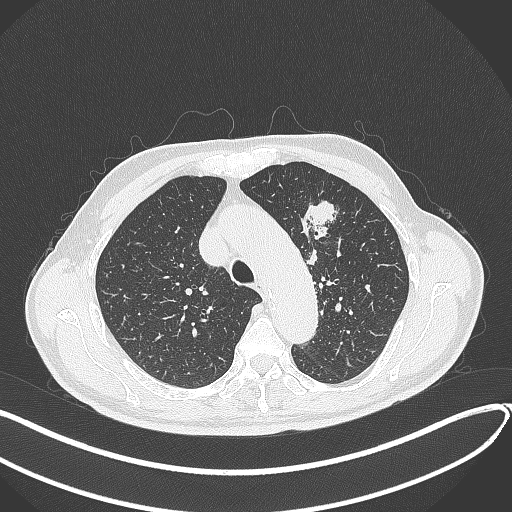
Chest CT, one axial slice; position 311 of 459 along the scan axis; reconstruction kernel B70f; lung window (W 1500 / L -600 HU); 1 mm slice thickness; 512 × 512 image matrix. Patient: male, 74 years. From the clinical record (not read from this slice): clinical TNM (as recorded): T2b N0 M1c.
Annotated regions visible in this slice (rectangle marked by the reading radiologist):
- lung tumour (recorded histology: adenocarcinoma): bounding box (x1, y1, x2, y2) in pixels: (299, 193, 345, 247)